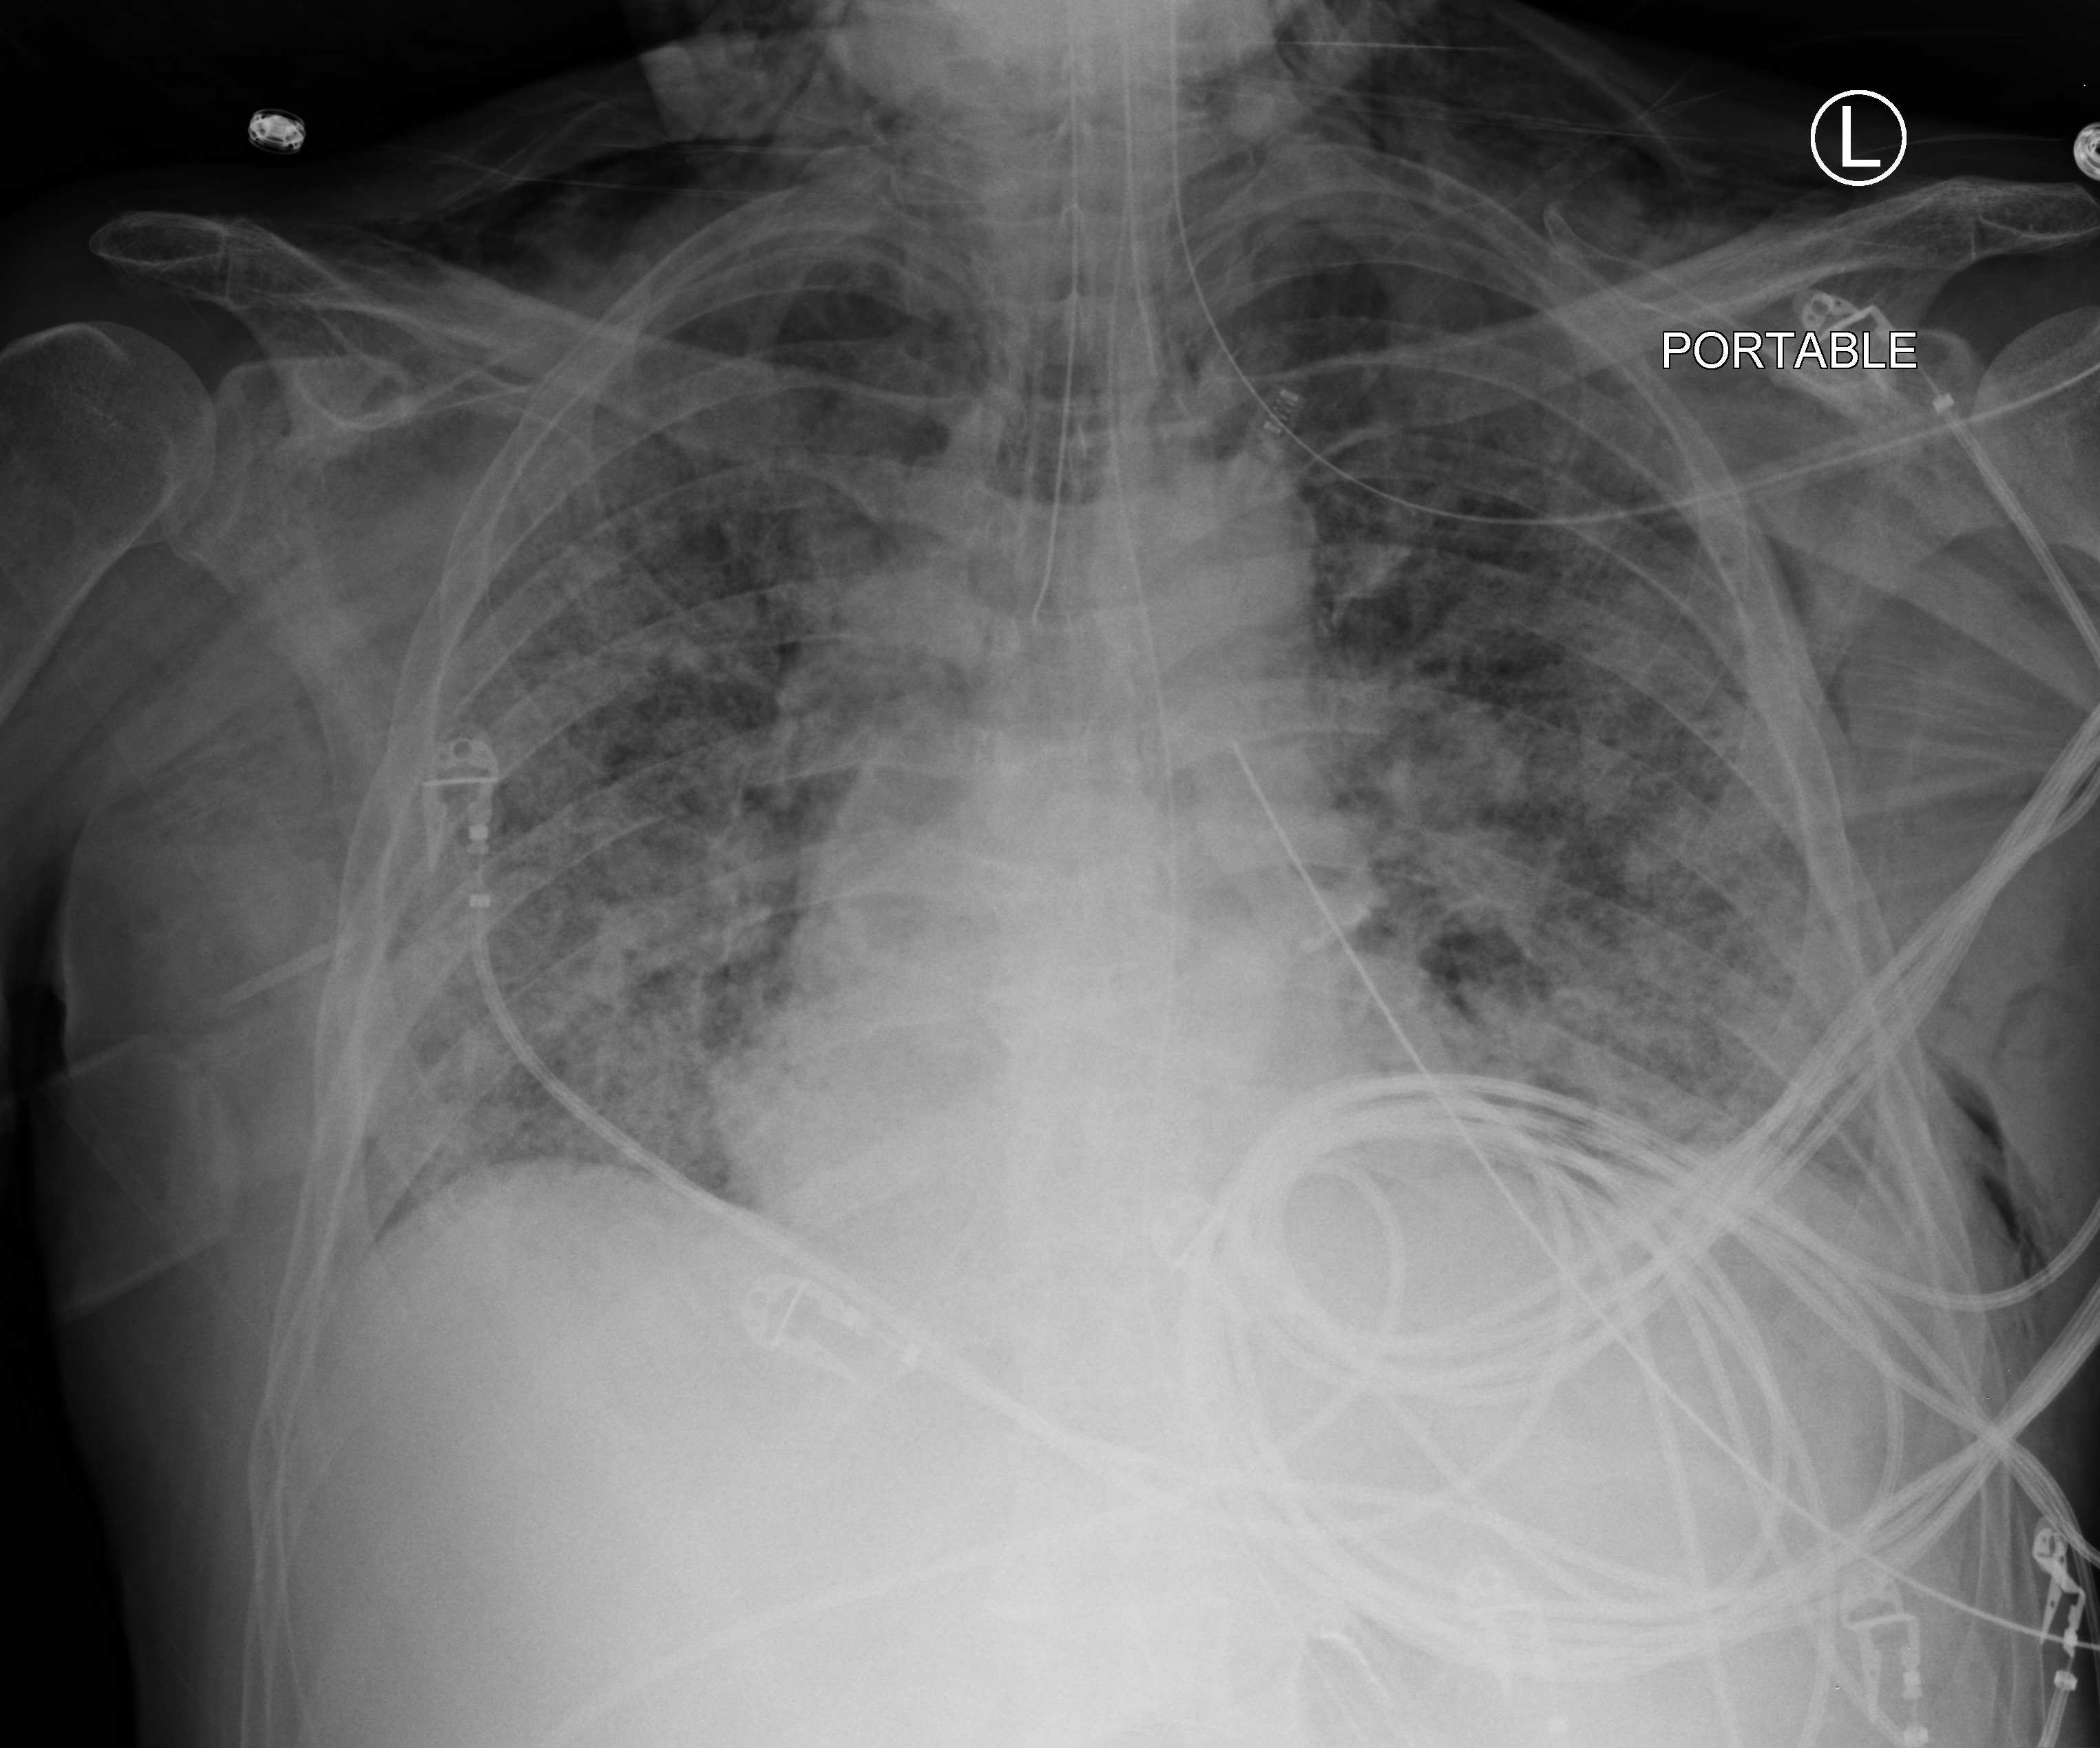
Portable chest radiograph; anteroposterior (AP) projection. Patient hospitalised with COVID-19; male, aged 60–74 years.
Hospital-stay facts (about this admission, not read from this image; timing relative to this image not recorded): mechanically ventilated during this hospital stay: yes; admitted to intensive care during this hospital stay: yes.